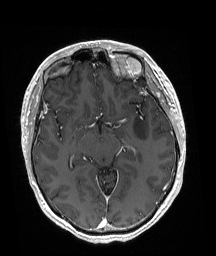
Brain MRI from a brain-tumour surgery series, one axial slice. T1-weighted post-contrast. 1 mm slice thickness. 216 × 256 image matrix. Case-level facts recorded for this patient, not image findings: histopathology: Astrocytoma; WHO grade: 3; IDH mutation: yes; tumour location: Left Posterior Frontal.
Annotated regions visible in this slice (expert manual segmentation):
- tumour: bounding box (x1, y1, x2, y2) in pixels: (133, 116, 147, 139)